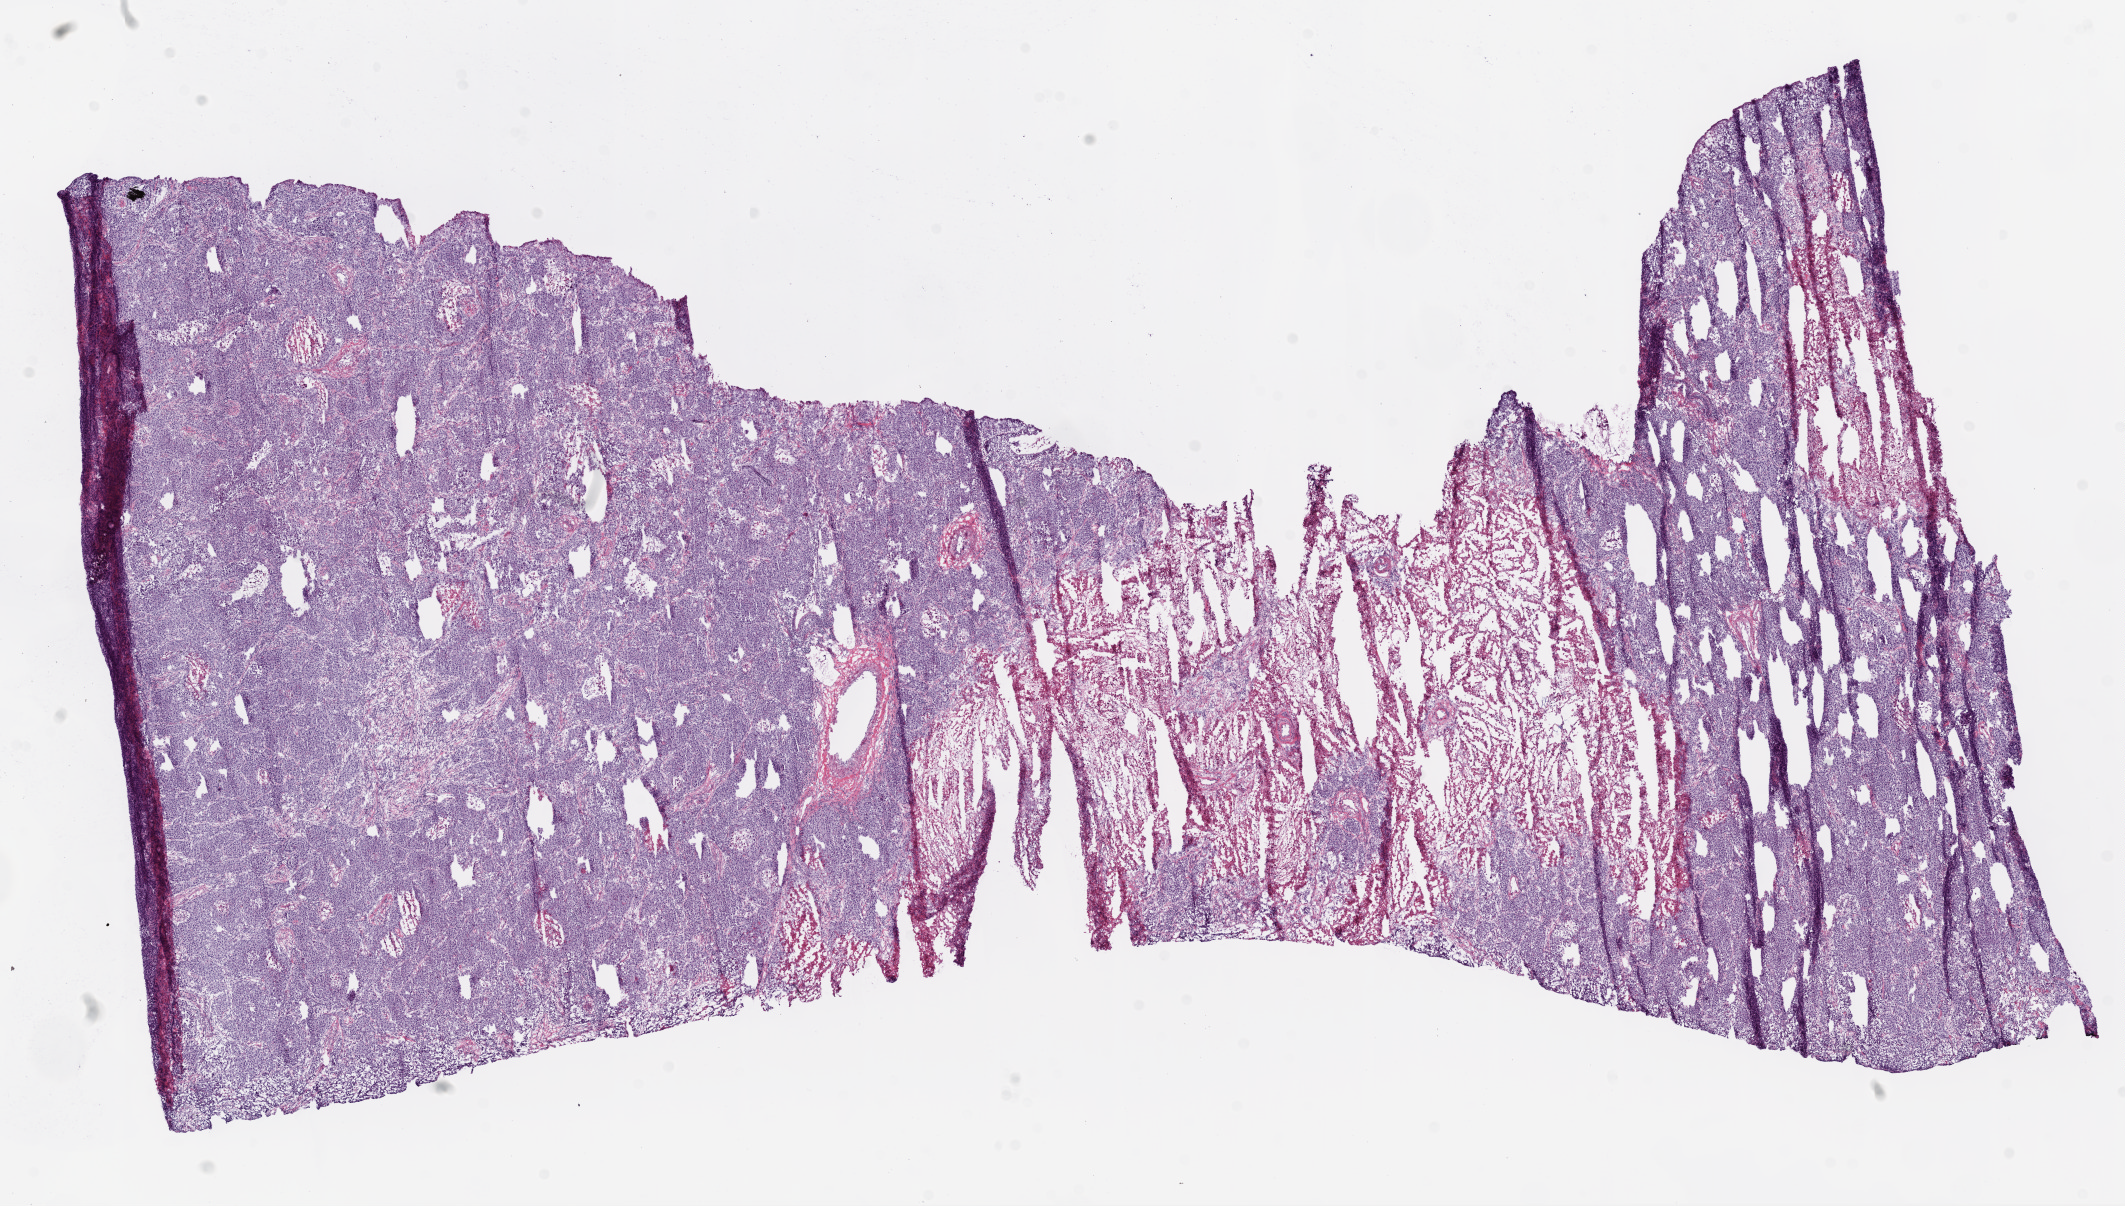
Digitized H&E tissue section (whole slide), shown as a low-resolution overview of the whole scanned area (about 17.1 x 9.7 mm), frozen section from the top of the tissue portion, sample: primary tumour, lung. Male, age 68 years at initial diagnosis. Composition of this section per pathologist review: tumour cells 70%, tumour nuclei 90%, normal cells 5%, stromal cells 5%, necrosis 20%.
Diagnosis: Adenocarcinoma, NOS (lower lobe, lung). AJCC pathologic stage: IIIA.